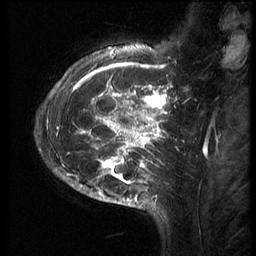
Breast MRI (dynamic contrast-enhanced), one sagittal slice; slice 19 of 70 in the series (ordered by position); 3 images stored at this slice position (order not interpretable as contrast timing); 1.5 T; TE 4.2 ms, TR 9 ms; 256 × 256 image matrix, field of view 180 × 180 mm. Patient: female, 28 years. From the clinical record (not read from this slice): setting: breast cancer imaged before/during neoadjuvant chemotherapy.
Structures marked on this image (semi-automatic segmentation, software-assisted and operator-edited):
- analysis volume of interest (the breast-tissue region the enhancement analysis was run in; not a lesion): box from (x=43, y=42) to (x=186, y=215) px
- tumour enhancement mask (voxels above the 140 % enhancement threshold inside the analysis volume of interest): (x=57, y=48)–(x=171, y=207)